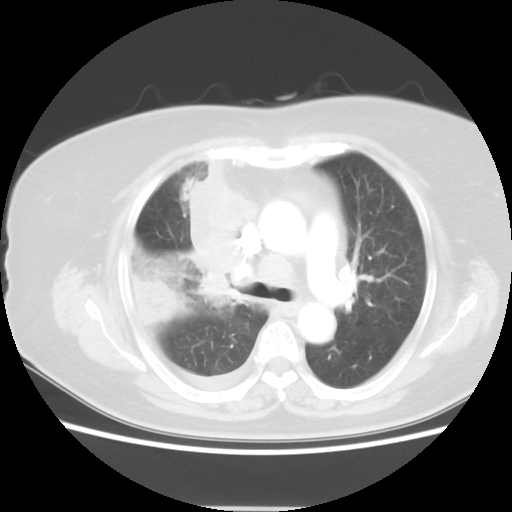
Chest CT, one axial slice; position 31 of 48 along the scan axis; 120 kVp; lung window (W 1500 / L -600 HU); 512 × 512 image matrix, field of view 360 × 360 mm. Female patient, age 73 years. Case-level facts recorded for this patient, not image findings: clinical TNM (as recorded): T3 N3 M1b; histopathological grade: G3.
Structures marked on this image (rectangle marked by the reading radiologist):
- lung tumour (recorded histology: small cell carcinoma): bounding box [x1, y1, x2, y2] px = [187, 156, 260, 293]